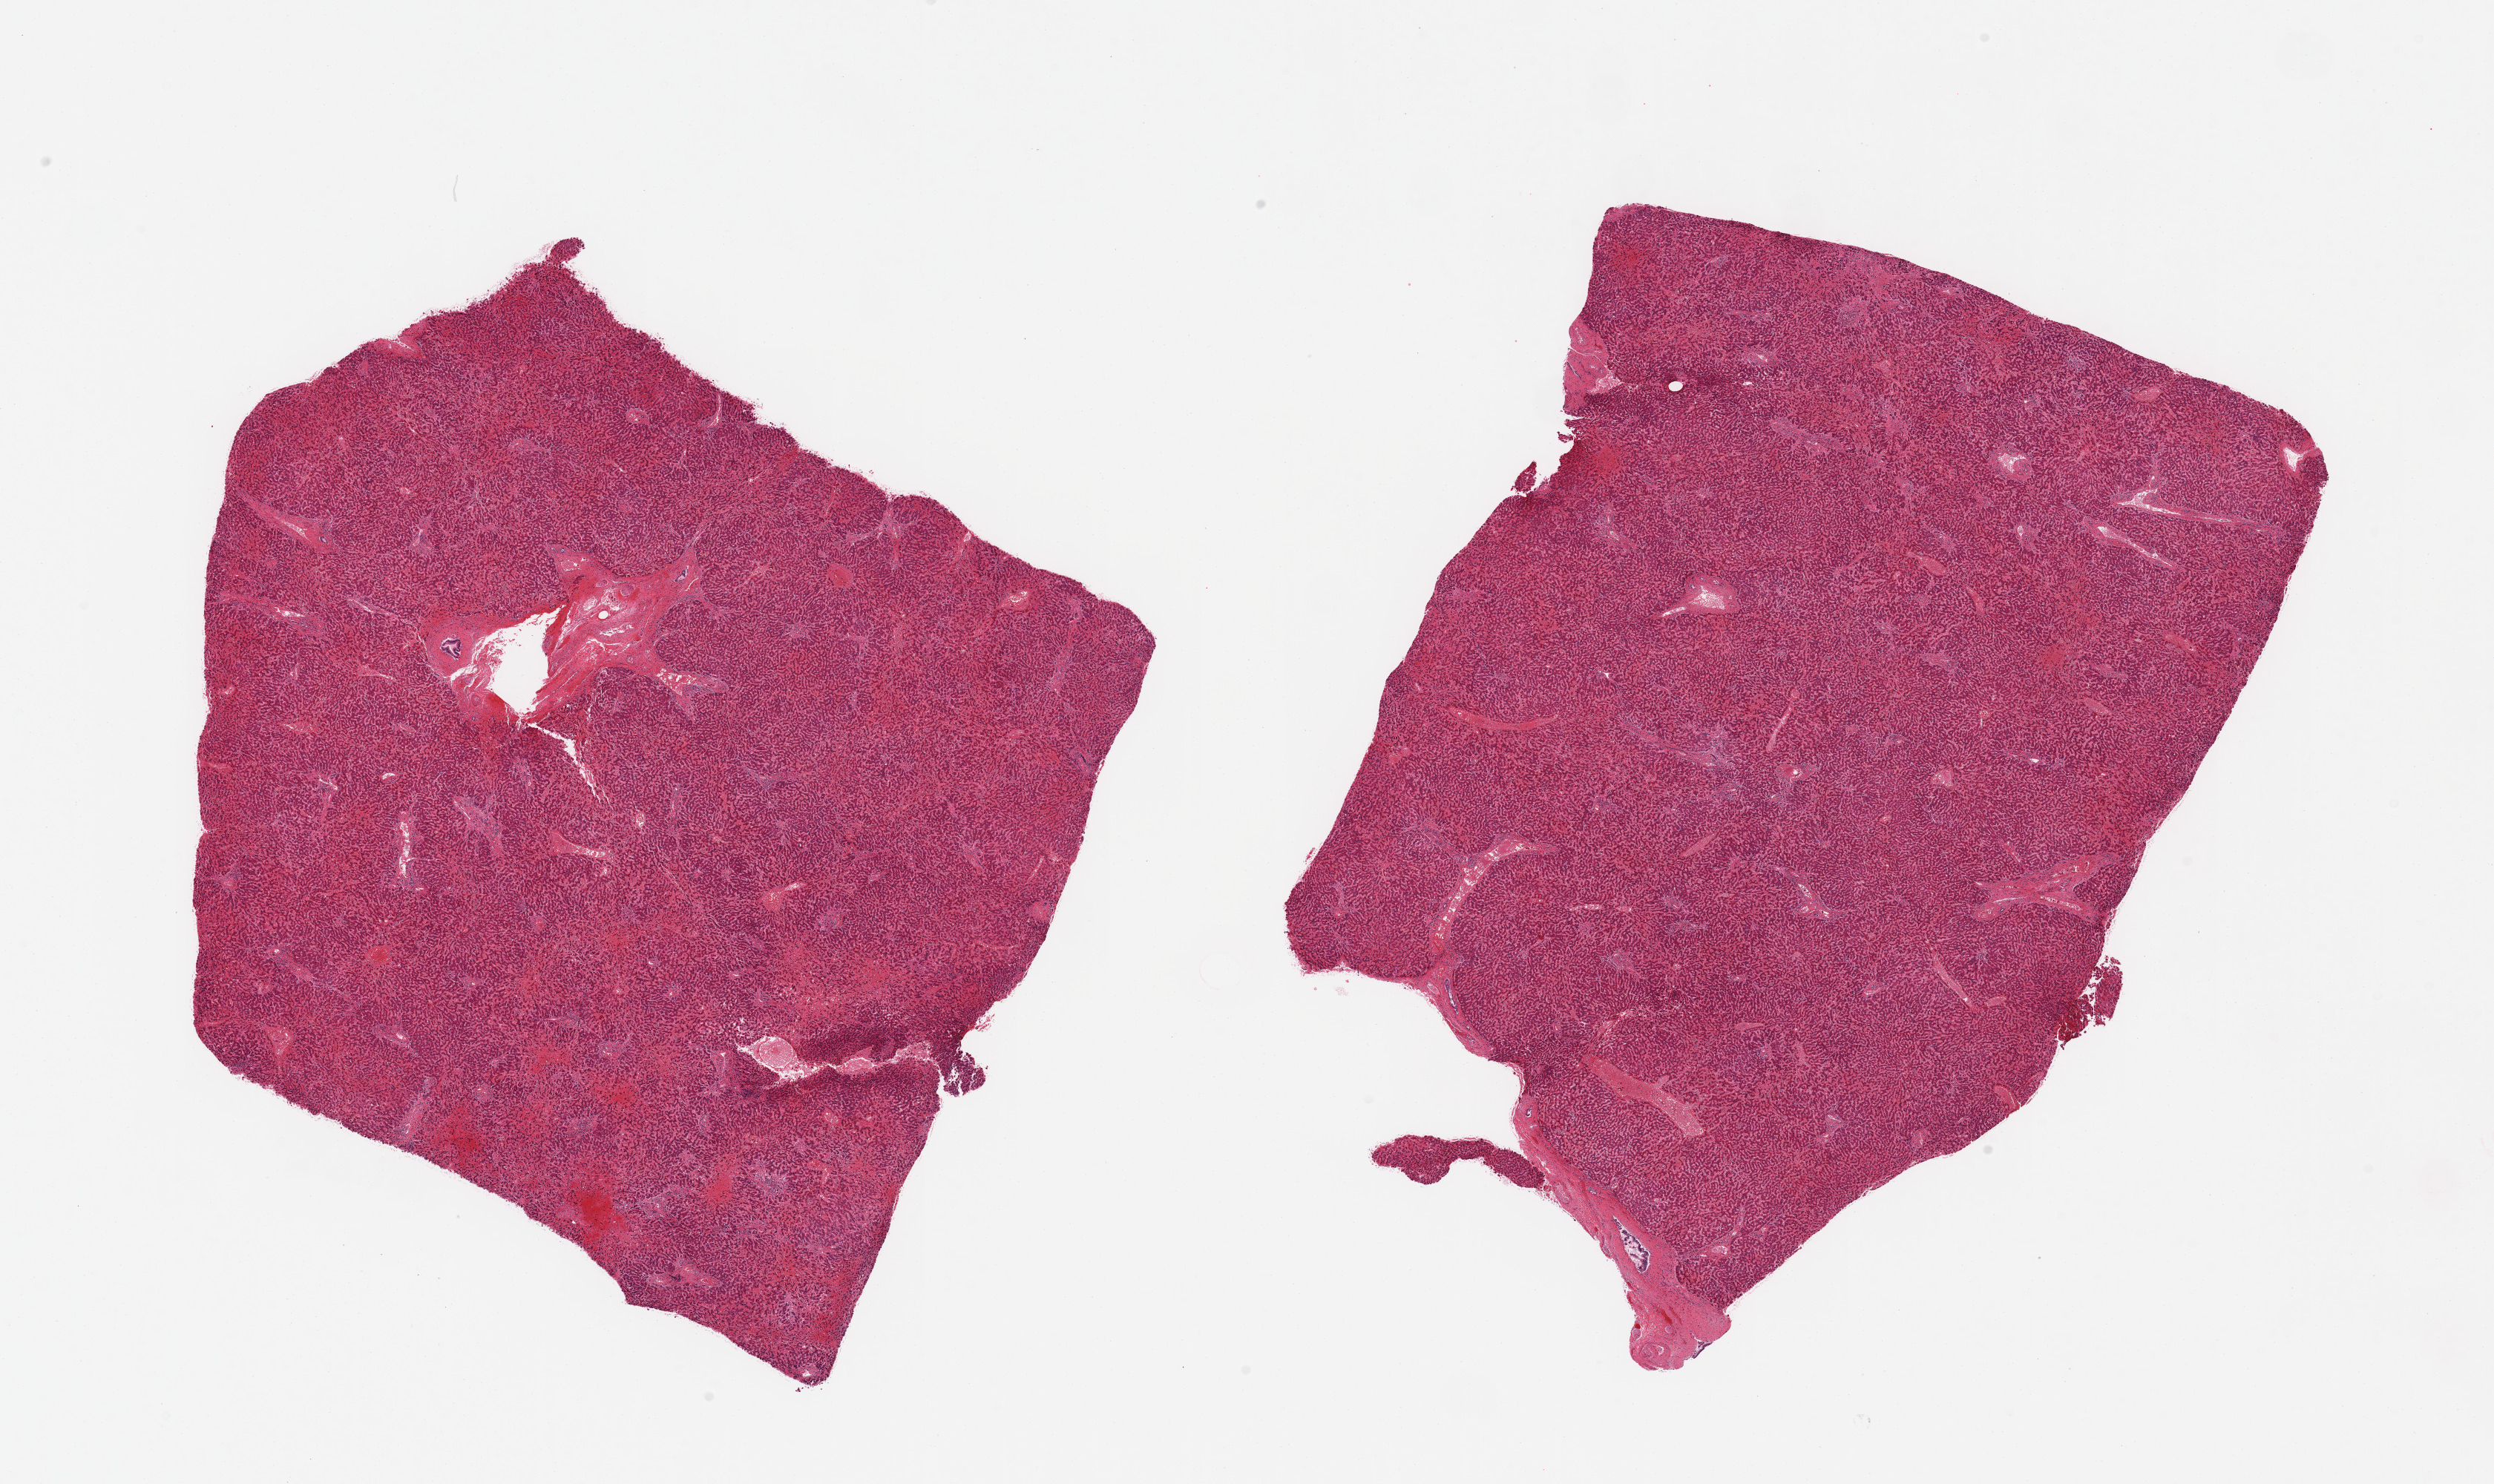
H&E whole-slide image — whole scanned area (about 26.6 x 15.8 mm, from a 20x scan) shown as a low-resolution overview, PAXgene-fixed paraffin-embedded (PFPE) section, section of liver (target tissue), donor tissue sample. Donor sex: male.
• reviewer comment on this tissue sample: 2 pieces, moderate passive congestion